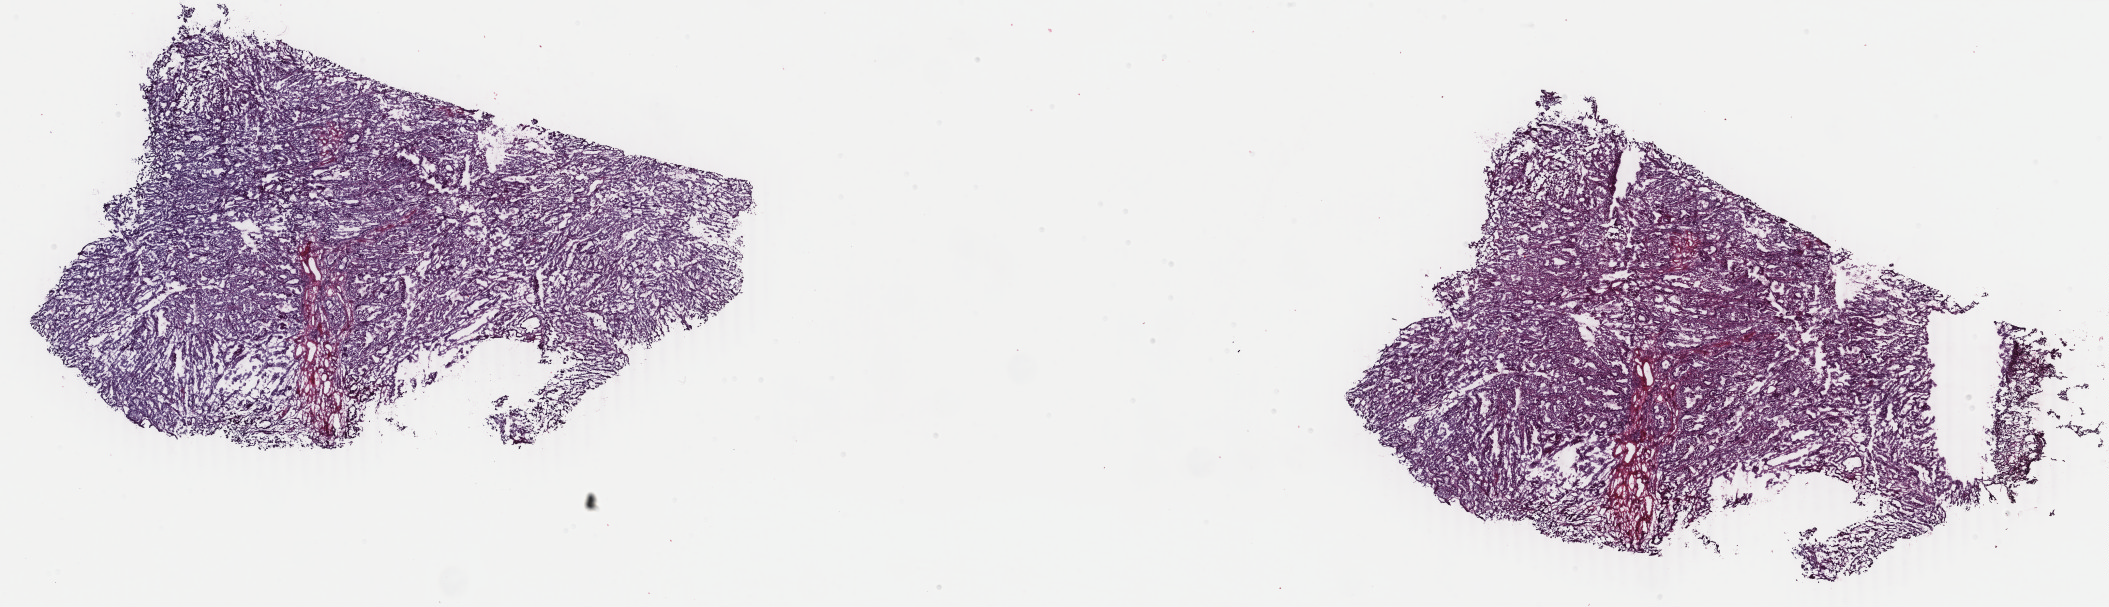
Whole-slide histology image, H&E — a low-resolution overview of the entire scanned area, about 33.6 x 9.7 mm (slide scanned at 40x), frozen section from the top of the tissue portion, uterus, primary tumour sample. Female patient; age at initial diagnosis 42 years. Histologic grade: G1 (well differentiated). Pathologist review of this section (percent, as recorded): tumour cells 100%, tumour nuclei 75%, normal cells 0%, stromal cells 0%, necrosis 0%. Inflammatory infiltration, as recorded: lymphocyte infiltration 0%, monocyte infiltration 0%, neutrophil infiltration 0%.
FIGO stage: IA. Pathologic diagnosis: Endometrioid adenocarcinoma, NOS (endometrium). Lymph nodes positive (case pathology): 0 of 14 examined.